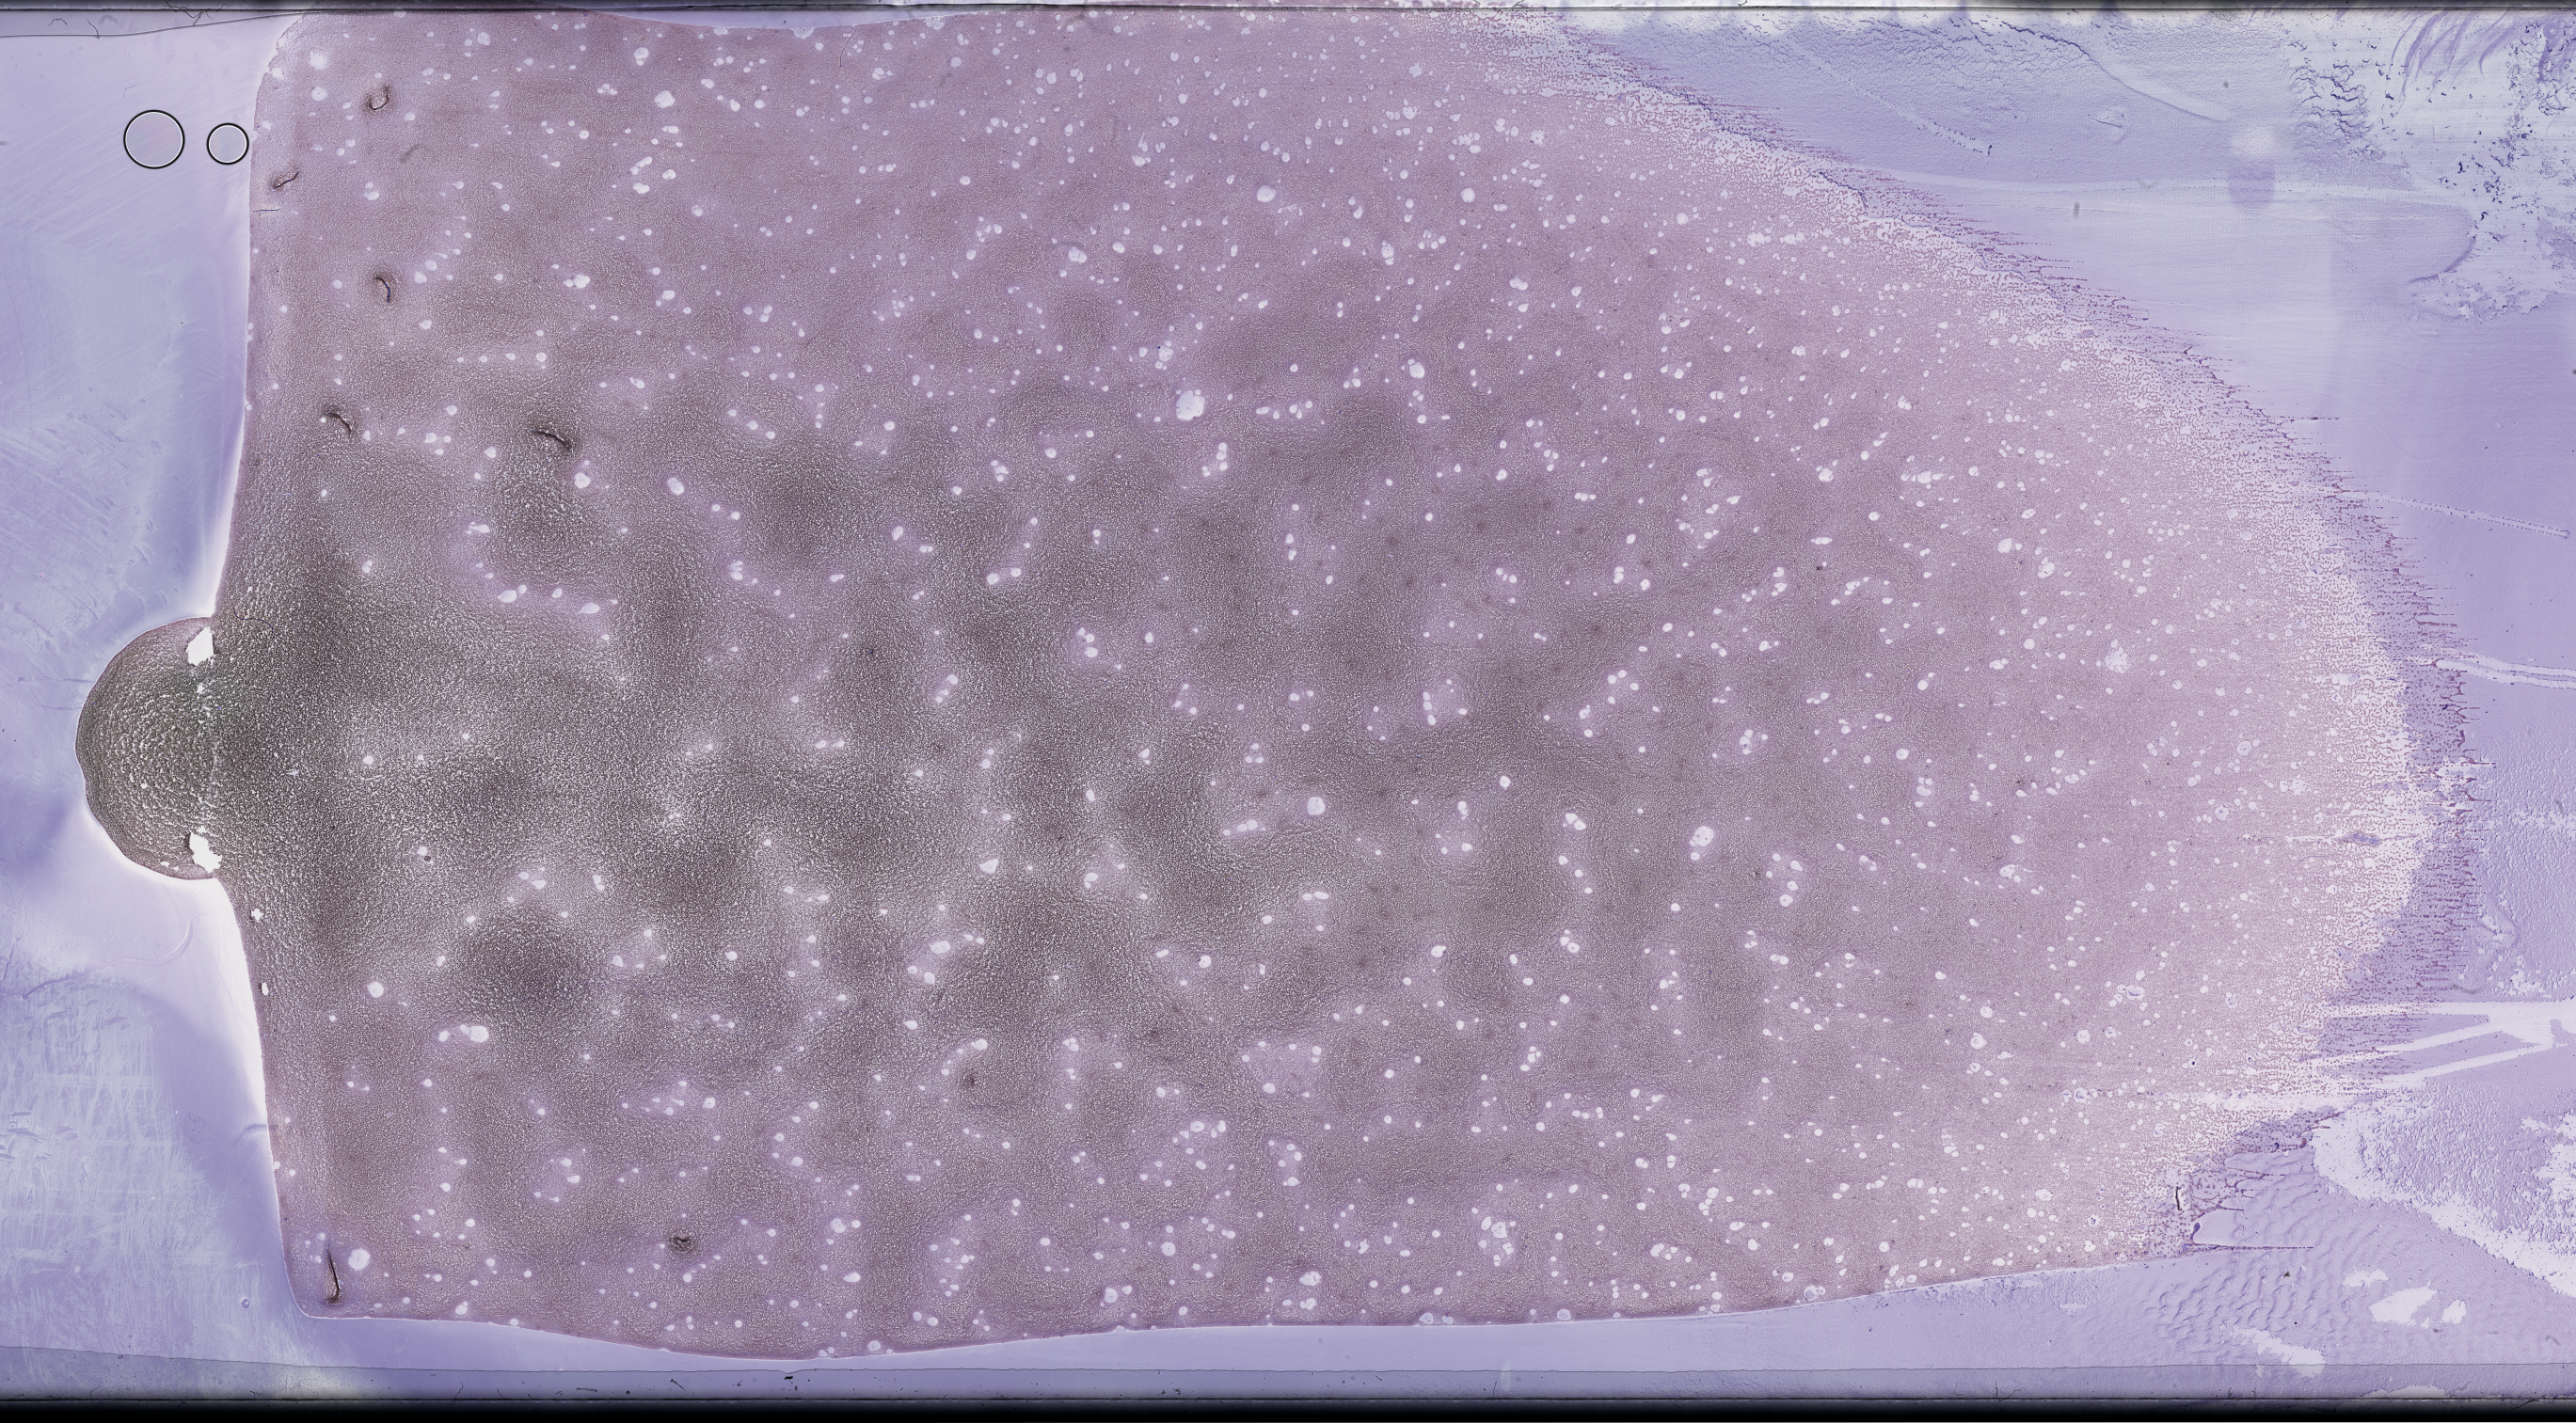
Wright–Giemsa-stained whole blood smear, whole-slide image, whole scanned area (about 44.2 x 24.4 mm) shown as a low-resolution overview. Patient: male.
From a patient with: Plasma Cell Myeloma.